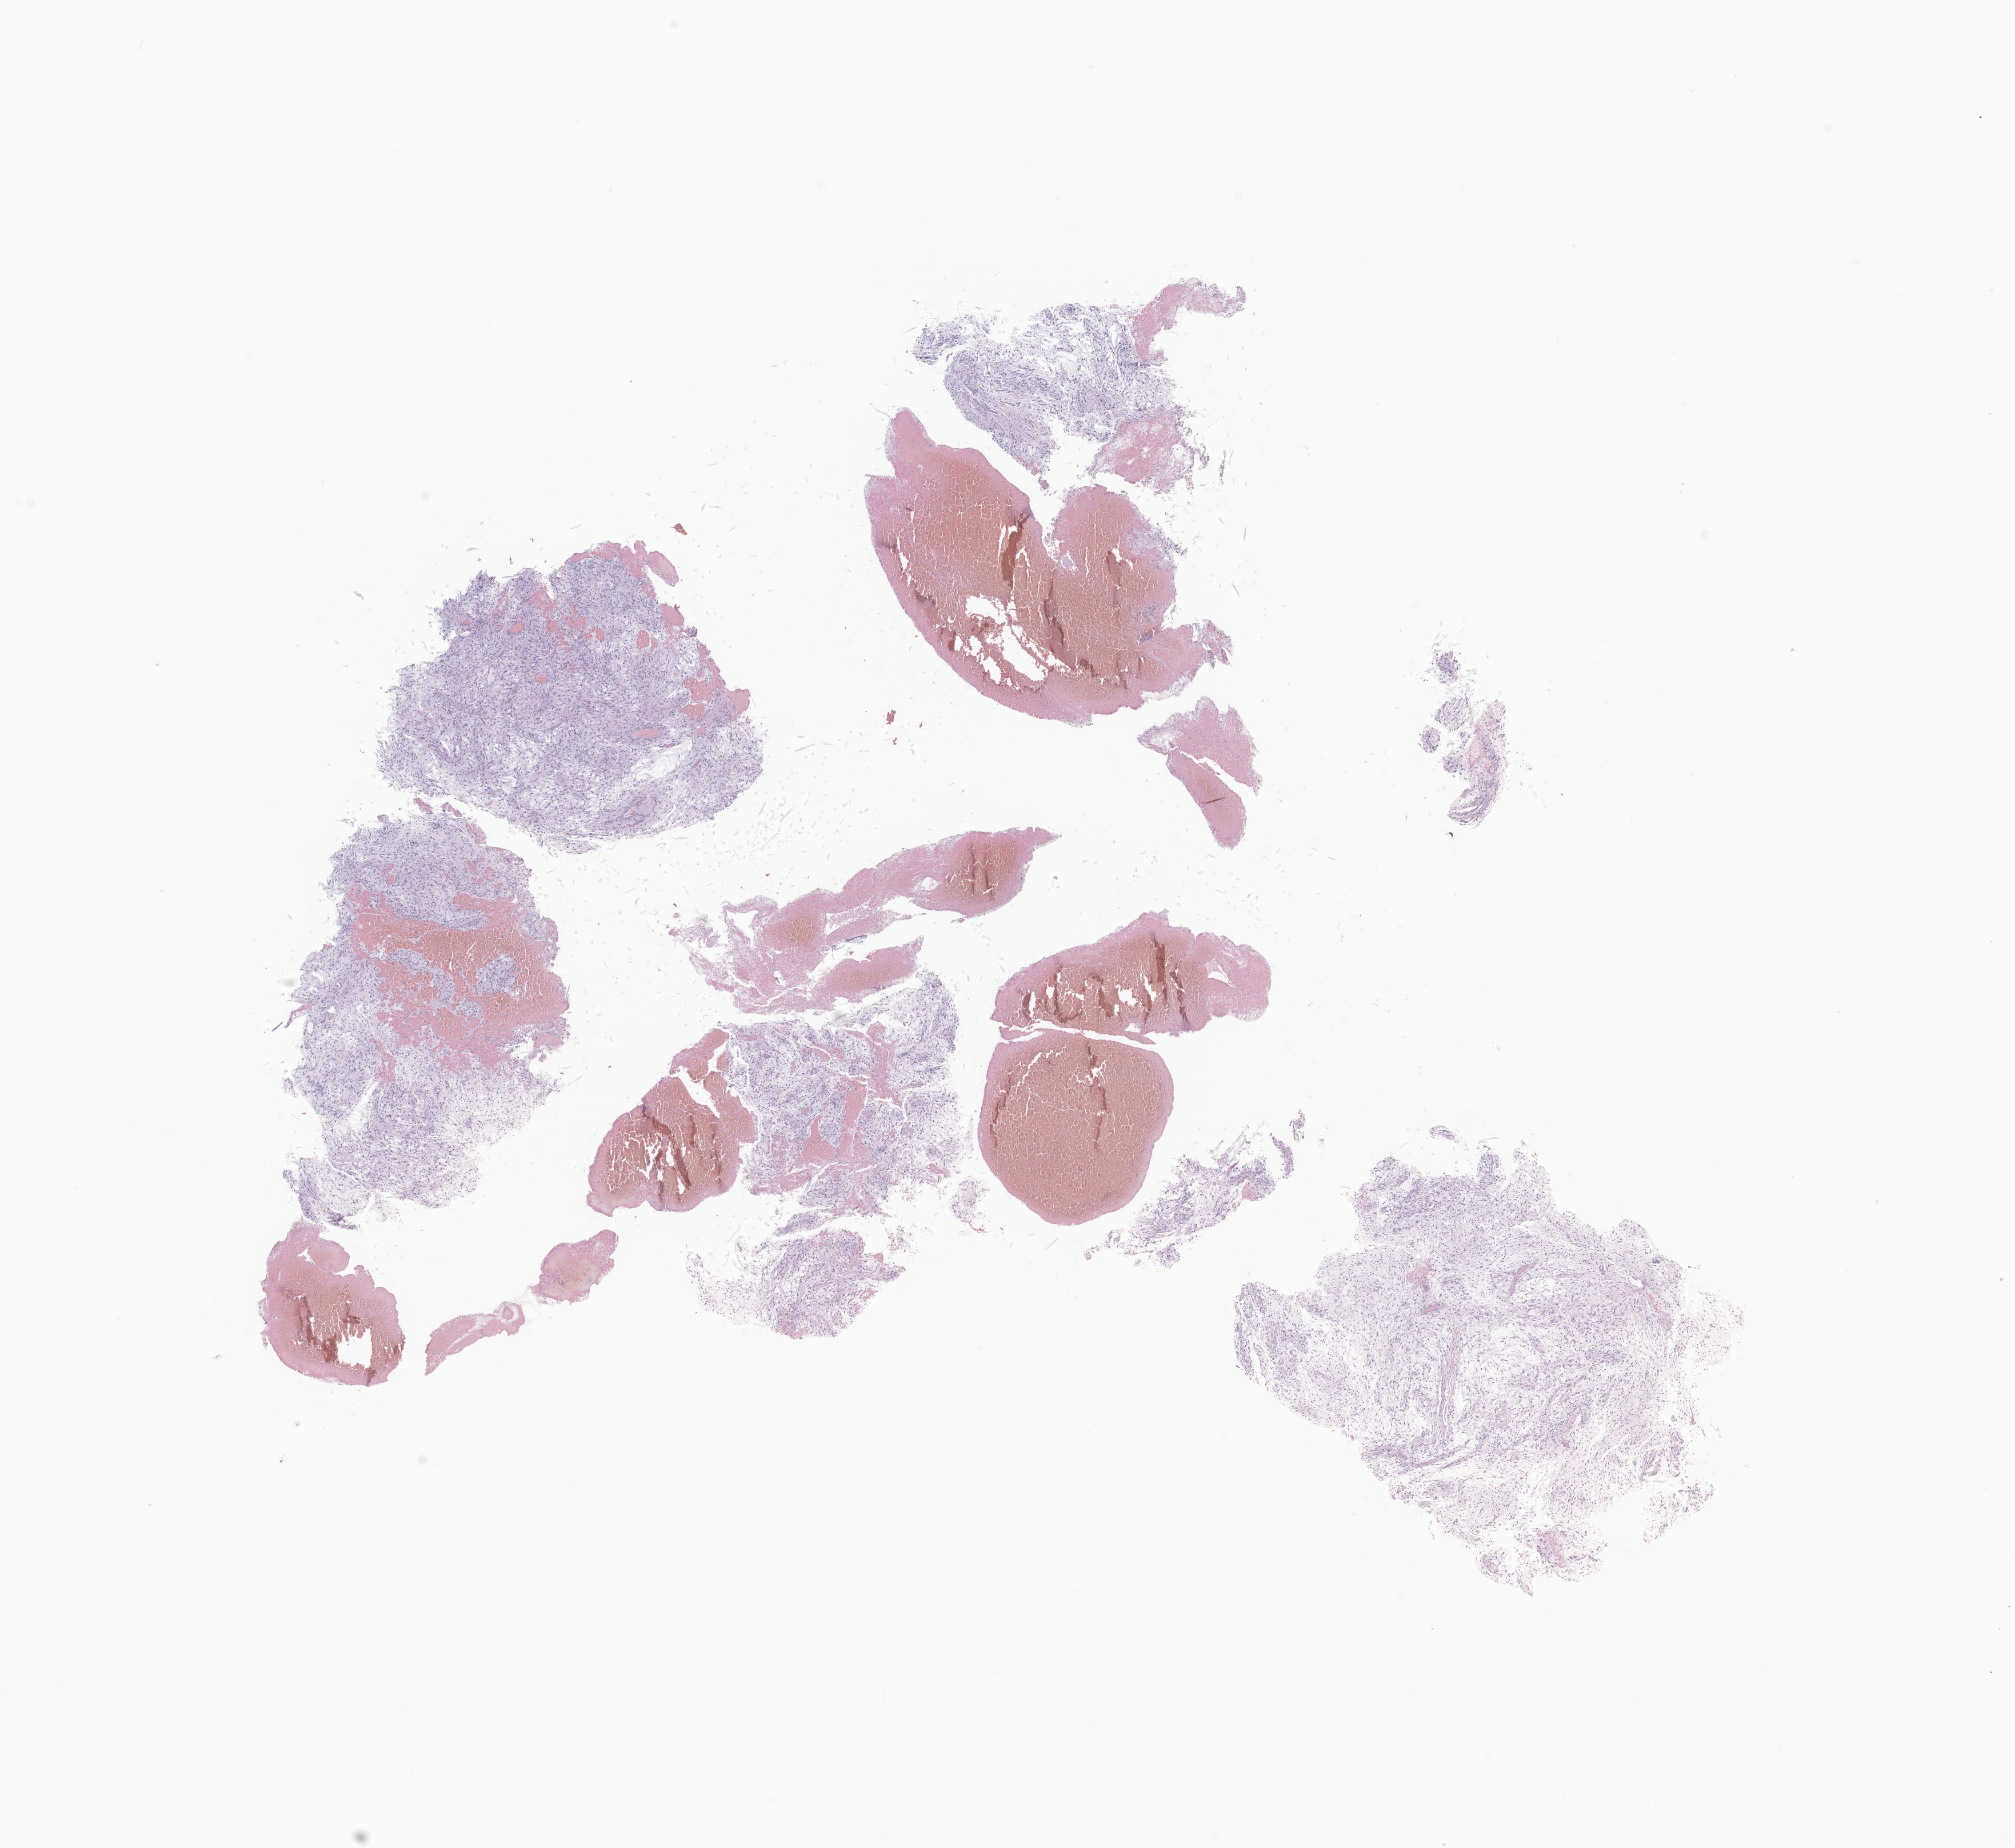
H&E whole-slide image of tumor tissue from the cerebral ventricle — whole scanned area (about 14.9 x 13.6 mm) shown as a low-resolution overview, formalin-fixed, paraffin-embedded (FFPE) tissue. Patient female; age 172 months.
Diagnosis: Pilocytic astrocytoma.